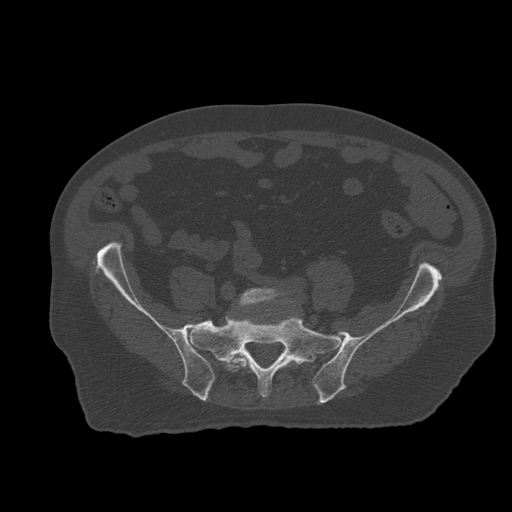
CT including the spine, one axial slice; slice 126 of 399 in the series (ordered by position); reconstruction kernel STANDARD; 120 kVp; bone window (W 1800 / L 400 HU); 1.25 mm slice thickness; 512 × 512 image matrix, field of view 407 × 407 mm. Patient age 73 years. Case-level facts recorded for this patient, not image findings: primary cancer: prostate; vertebrae with lytic lesions (as recorded): L2.
Outlined on this slice (semi-automatic segmentation, software-assisted and operator-edited):
- L5 vertebra: bounding box [x1, y1, x2, y2] px = [225, 288, 296, 373]